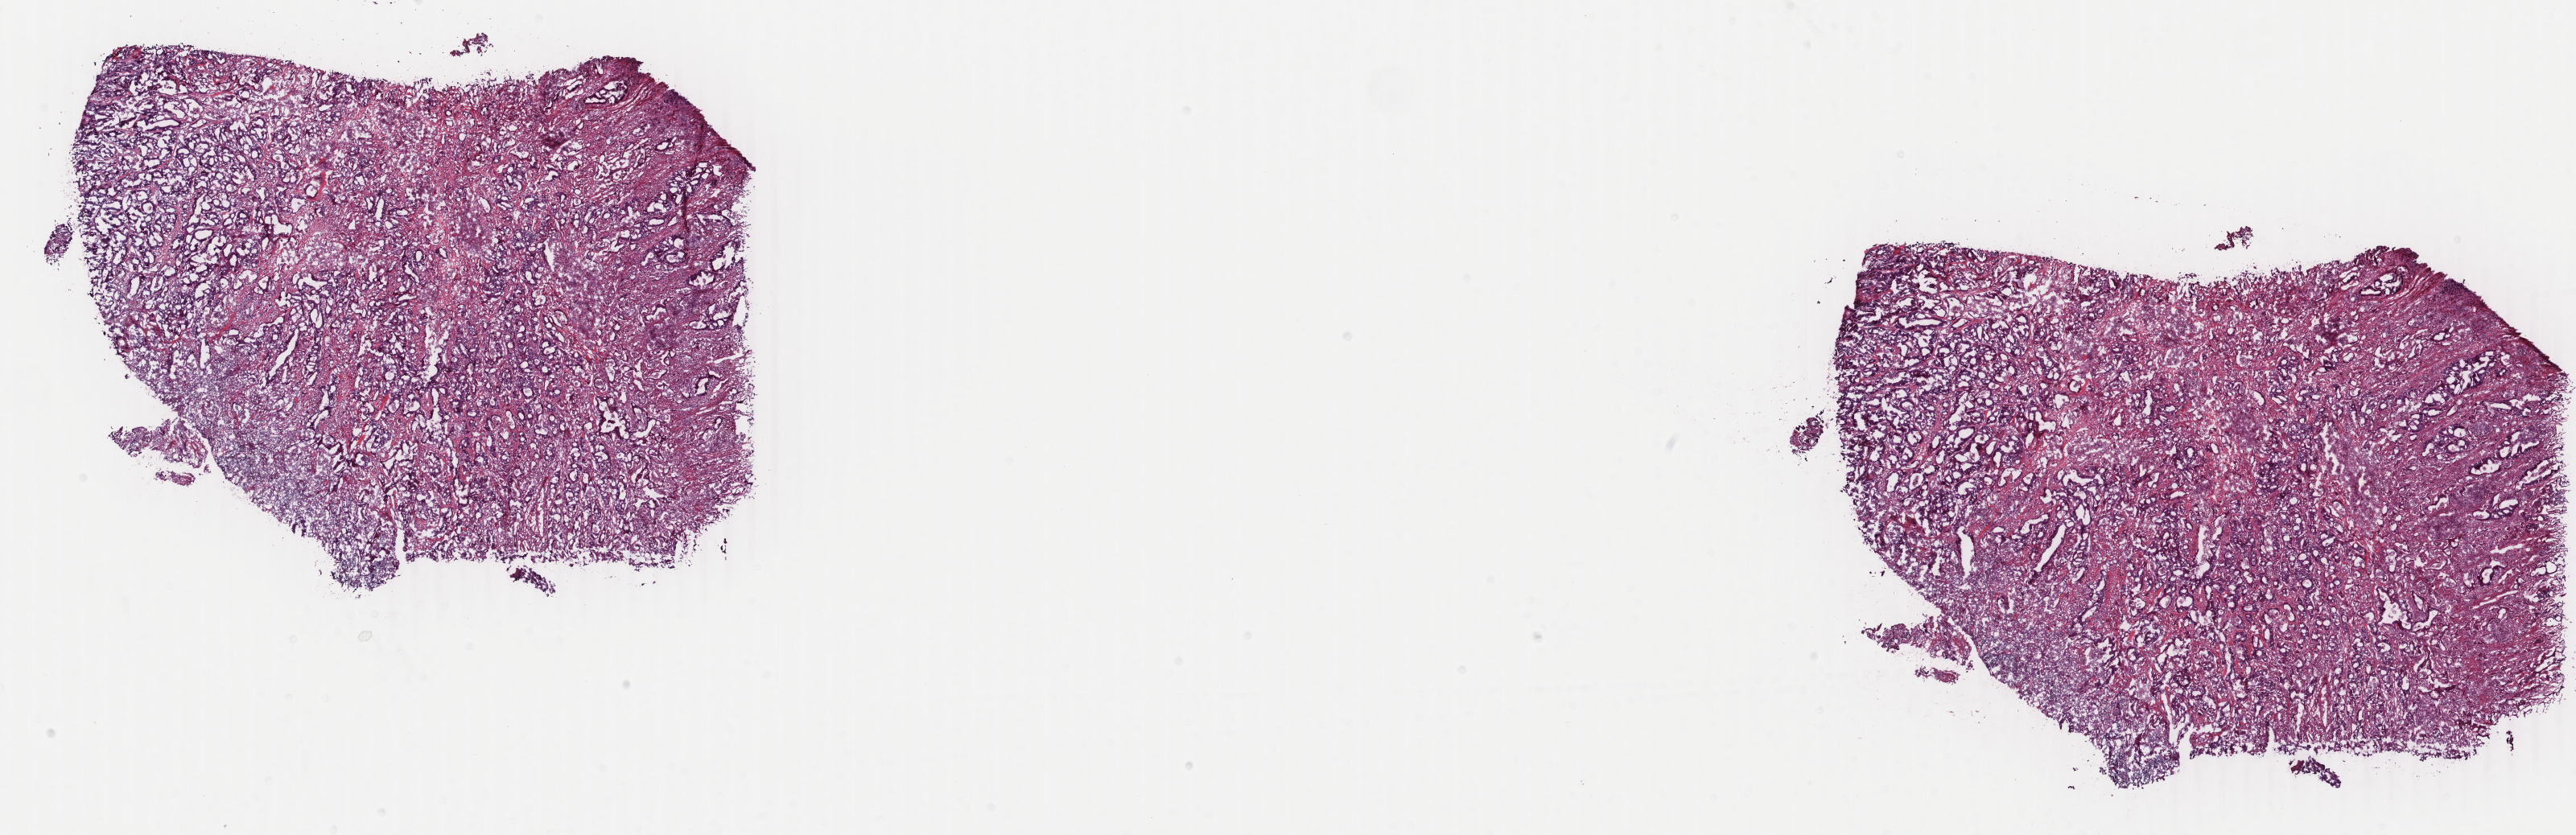
Digitized Hematoxylin and eosin (H&E) stained tissue section (whole slide) — whole scanned area (about 25.5 x 8.3 mm, acquisition: 40x scan) shown as a low-resolution overview, frozen section, primary tumour sample from the colon. Male, age 65 years at initial diagnosis. Composition of this section per pathologist review: tumour cells 75%, tumour nuclei 65%, normal cells 0%, stromal cells 15%, necrosis 10%. Infiltration values recorded for this section: lymphocyte infiltration 2%, monocyte infiltration 1%, neutrophil infiltration 20%.
• lymph nodes positive (case pathology): 0 of 11 examined
• pathologic diagnosis: Adenocarcinoma, NOS (cecum)
• AJCC pathologic stage: IIA